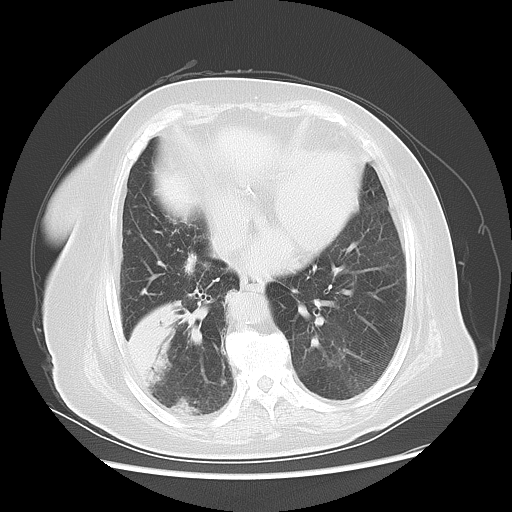
Chest CT, one axial slice; 120 kVp; lung window (W 1500 / L -600 HU); 5 mm slice thickness; 512 × 512 image matrix. Female patient, age 73 years. Case-level facts recorded for this patient, not image findings: clinical TNM (as recorded): T3 N0 M0.
Structures marked on this image (bounding box drawn by a radiologist):
- lung tumour (recorded histology: adenocarcinoma): bounding box [x1, y1, x2, y2] px = [120, 293, 185, 392]